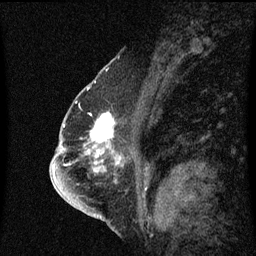
Breast MRI (dynamic contrast-enhanced), one sagittal slice. Dynamic contrast-enhanced series, image 2 of 3 at this slice position (ordered by acquisition). 1.5 T. TE 4.2 ms, TR 8.4 ms. 256 × 256 image matrix, field of view 200 × 200 mm. Patient: female, 57 years. From the clinical record (not read from this slice): setting: breast cancer imaged before/during neoadjuvant chemotherapy; receptor status: HR-positive, HER2-negative.
Outlined on this slice (semi-automatic segmentation, software-assisted and operator-edited):
- analysis volume of interest (the breast-tissue region the enhancement analysis was run in; not a lesion): bounding box <82,114,128,145> (left, top, right, bottom; pixels)
- tumour enhancement mask (voxels above the 70 % enhancement threshold inside the analysis volume of interest): <92,114,115,143>